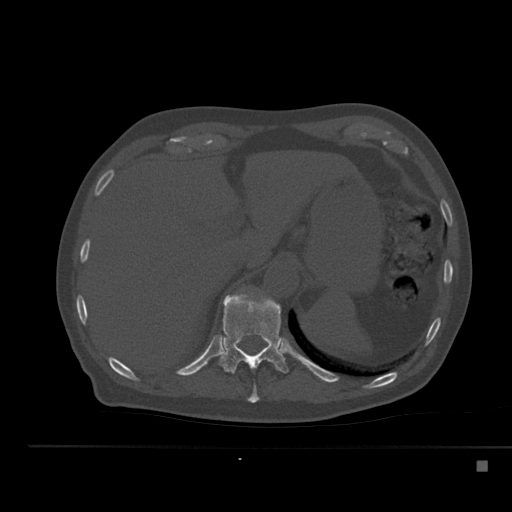
CT including the spine, one axial slice. Reconstruction kernel Br40s. Bone window (W 1800 / L 400 HU). 512 × 512 image matrix, field of view 408 × 408 mm. Patient: male, 70 years. From the clinical record (not read from this slice): primary cancer: renal; vertebrae with lytic lesions (as recorded): T4, T6, T10, T12, L3, L4, L5.
Annotated regions visible in this slice (semi-automatically segmented with operator editing):
- T10 vertebra: bounding box <247,384,259,403> (left, top, right, bottom; pixels)
- T11 vertebra: <219,293,289,374>